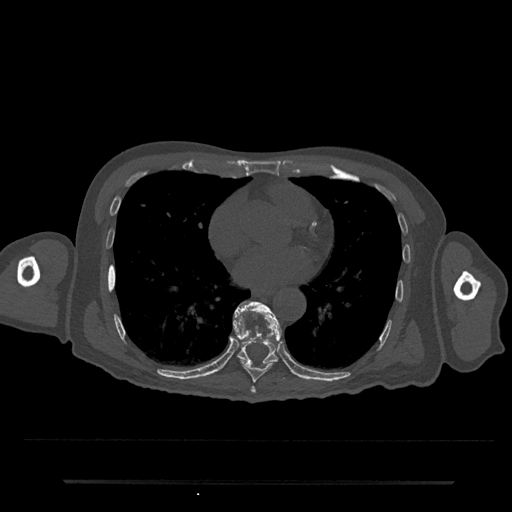
CT including the spine, one axial slice. Slice 398 of 797 in the series (ordered by position). 120 kVp. Bone window (W 1800 / L 400 HU). 0.5 mm slice thickness. 512 × 512 image matrix, field of view 427 × 427 mm. Male patient, age 74 years. Case-level facts recorded for this patient, not image findings: primary cancer: prostate.
Outlined on this slice (semi-automatic segmentation, software-assisted and operator-edited):
- T7 vertebra: bounding box <250,387,256,394> (left, top, right, bottom; pixels)
- T8 vertebra: <234,320,277,383>
- T9 vertebra: <233,301,282,364>